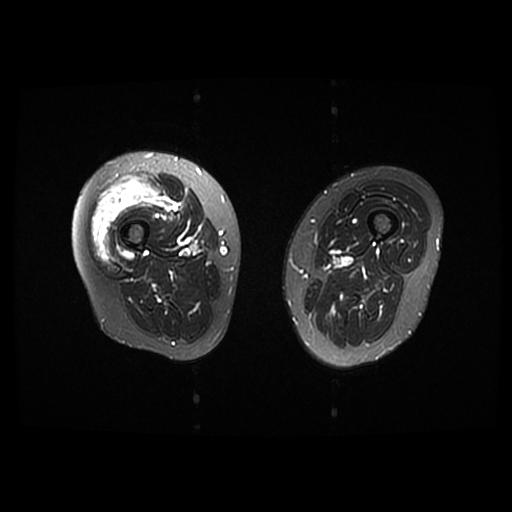
MRI of an extremity soft-tissue mass, one axial slice; position 10 of 42 along the scan axis; T2-weighted fat-saturated; 512 × 512 image matrix, field of view 440 × 440 mm. Female patient. Case-level facts recorded for this patient, not image findings: histological type: pleiomorphic undifferentiated sarcoma; grade: high; site of the primary tumour: right quadricep.
Outlined on this slice (manually delineated by an expert):
- gross tumour volume including surrounding oedema: bounding box (x1, y1, x2, y2) in pixels: (92, 175, 173, 259)